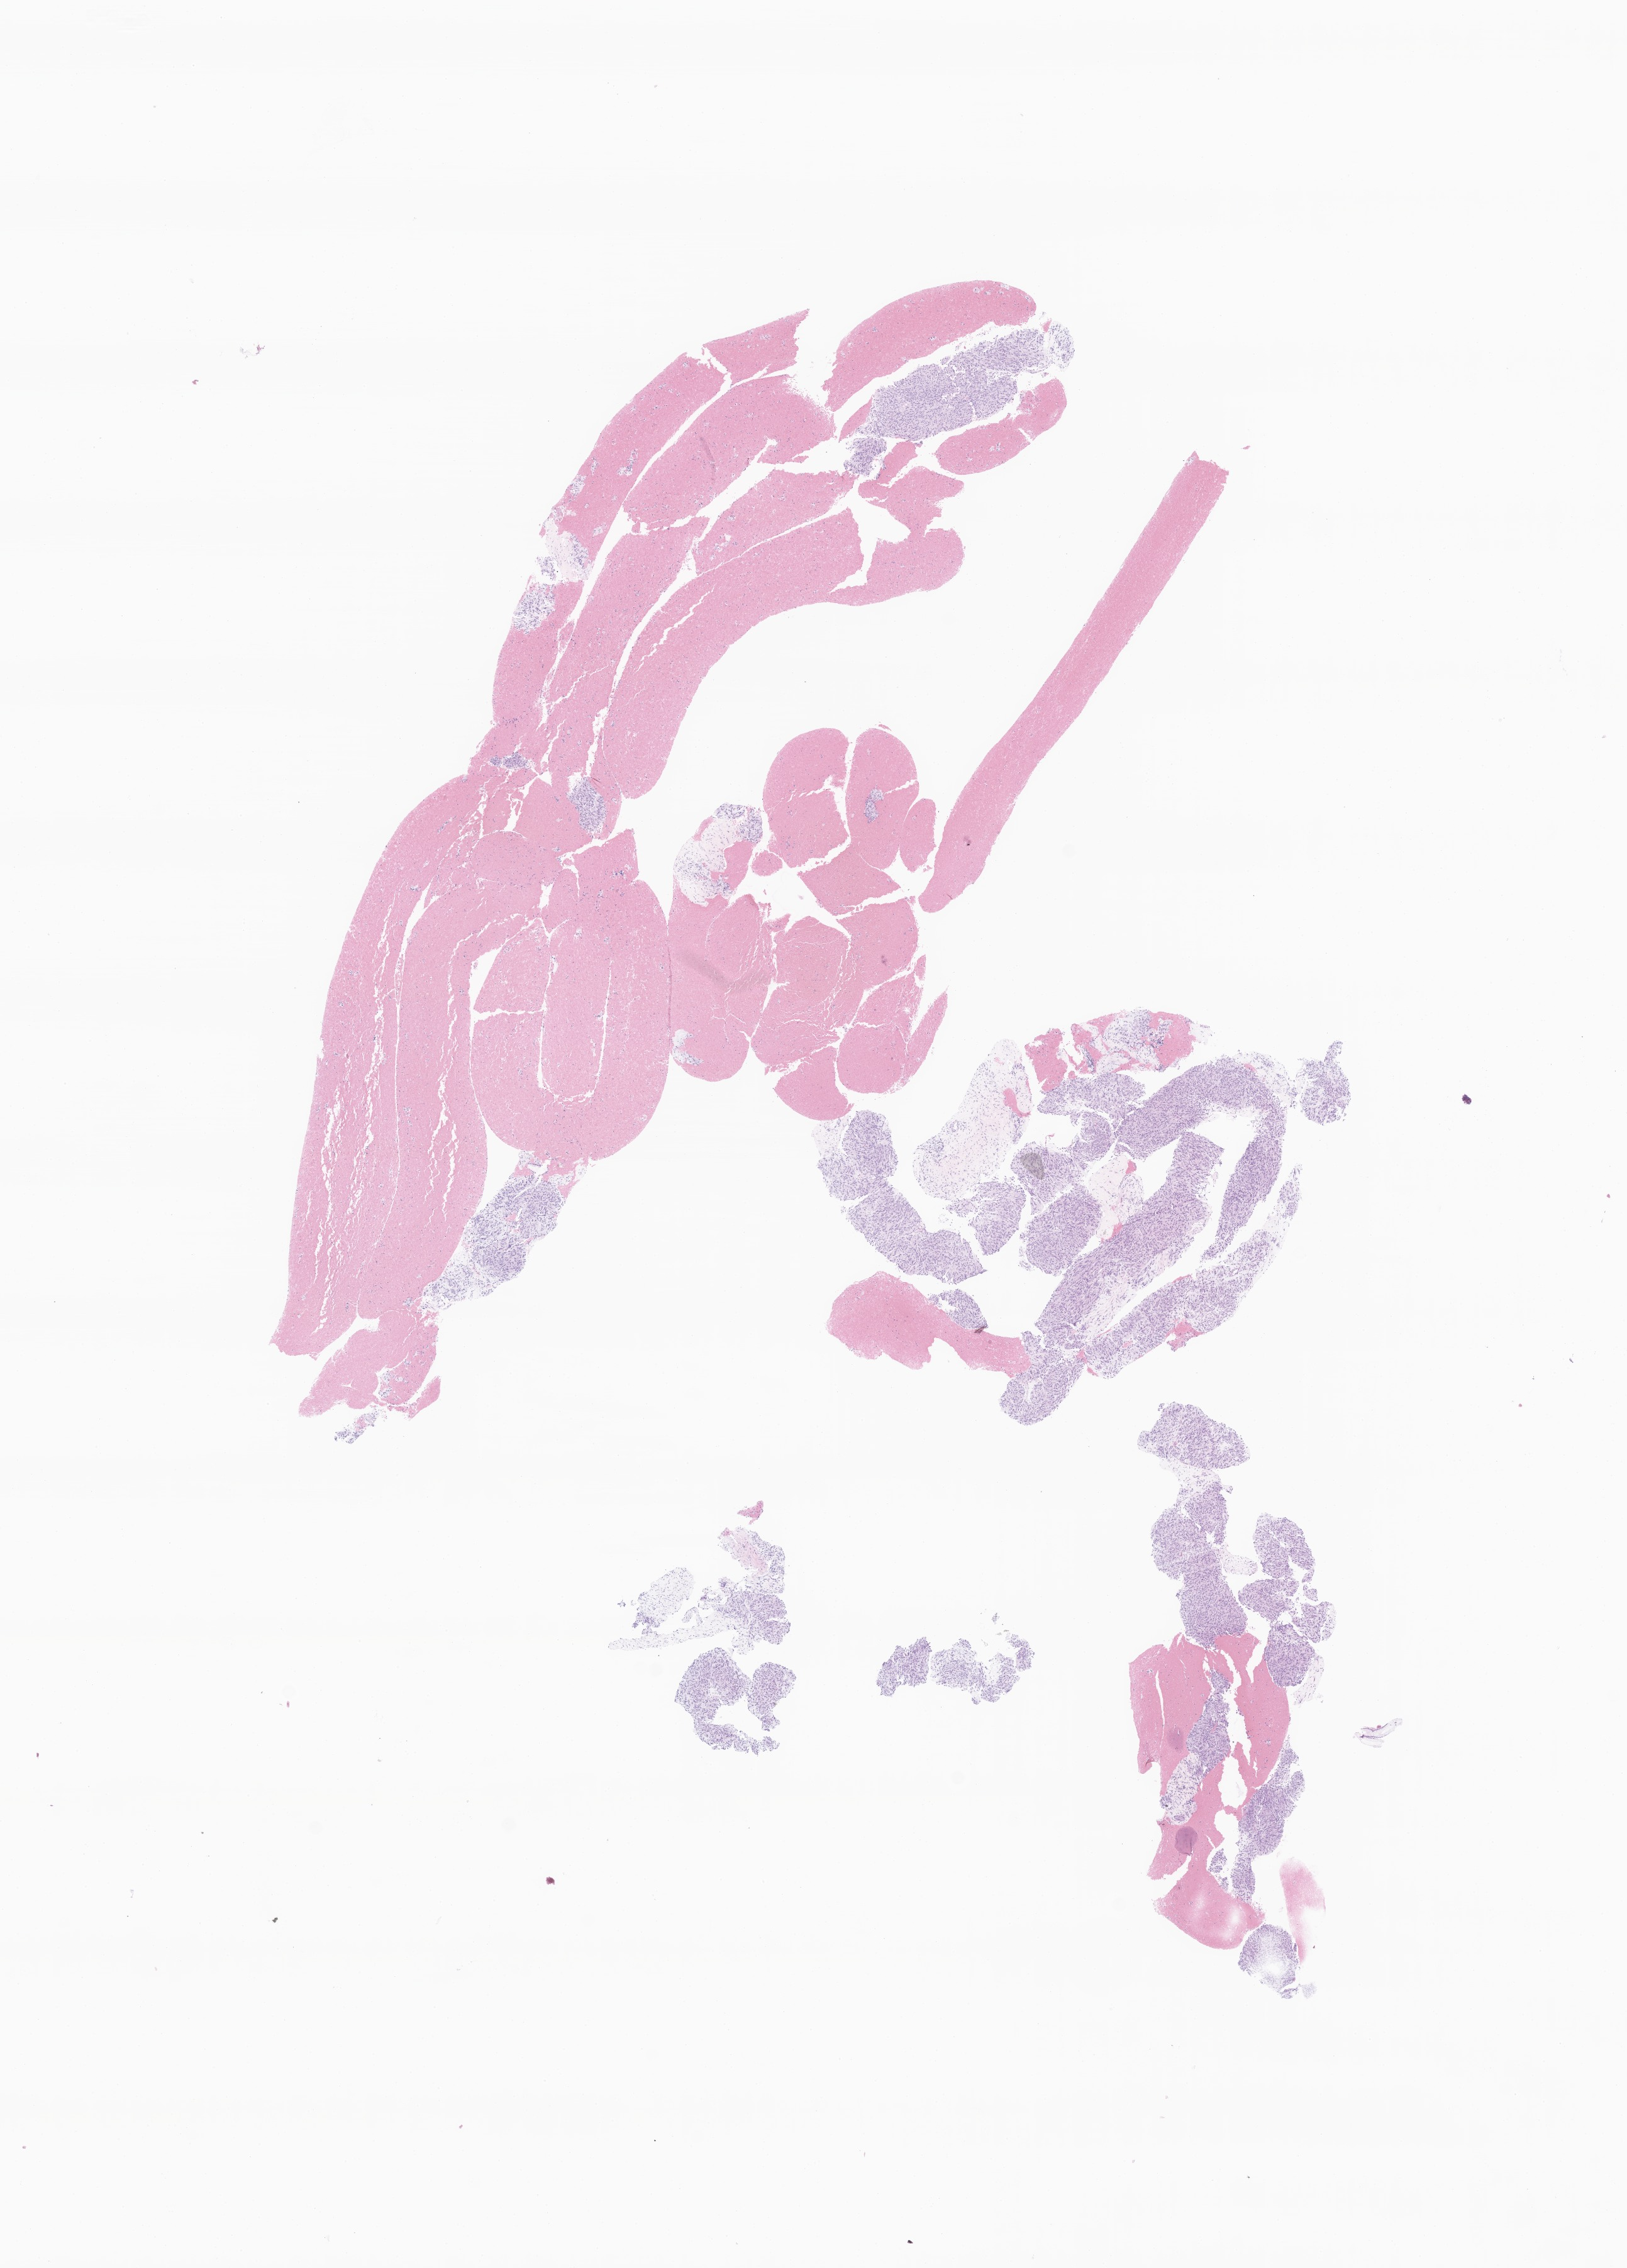
Whole-slide image, hematoxylin and eosin (H&E) stain of tumor tissue from the gastrointestinal tract — whole scanned area (about 10.9 x 15.2 mm) shown as a low-resolution overview; formalin-fixed, paraffin-embedded (FFPE) tissue. Patient female; age 197 months (16 years 5 months).
Diagnosis (ICD-O-3 morphology term): Gastrointestinal stromal tumor, NOS.